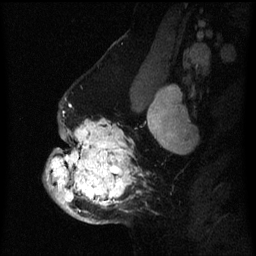
Breast MRI (dynamic contrast-enhanced), one sagittal slice; position 44 of 60 along the scan axis; dynamic contrast-enhanced series, image 2 of 3 at this slice position (ordered by acquisition); 1.5 T; TE 4.2 ms, TR 8 ms; 256 × 256 image matrix, field of view 190 × 190 mm. Patient: female, 50 years.
Annotated regions visible in this slice (semi-automatically segmented with operator editing):
- analysis volume of interest (the breast-tissue region the enhancement analysis was run in; not a lesion): box from (x=43, y=103) to (x=160, y=224) px
- tumour enhancement mask (voxels above the 70 % enhancement threshold inside the analysis volume of interest): (x=46, y=120)–(x=137, y=220)